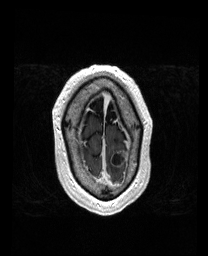
Brain MRI from a brain-tumour surgery series, one axial slice; position 156 of 192 along the scan axis; T1-weighted post-contrast; 1 mm slice thickness; 208 × 256 image matrix, field of view 211 × 260 mm. From the clinical record (not read from this slice): histopathology: Metastatic Carcinoma from Lung Adenocarcinoma.
Outlined on this slice (expert manual segmentation):
- tumour: box from (x=112, y=152) to (x=124, y=165) px